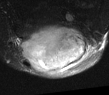
MRI of an extremity soft-tissue mass, one axial slice. T2-weighted fat-saturated. MR volume resampled by the dataset authors to the PET/CT grid (not the native acquisition matrix). 109 × 95 image matrix. Male patient. Case-level facts recorded for this patient, not image findings: histological type: synovial sarcoma; site of the primary tumour: left poplietal fossa.
Outlined on this slice (expert contour drawn on MRI and transferred to this co-registered scan by the dataset authors):
- gross tumour volume (mass): bounding box <17,26,89,75> (left, top, right, bottom; pixels)